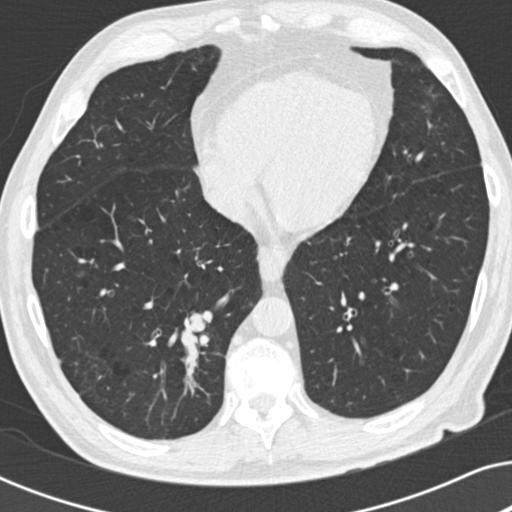
Low-dose screening chest CT, axial slice; baseline screening round; lung window (W 1500 / L -600 HU); 2 mm slice thickness; slice 112 of 191 in the series; 512 × 512 image matrix. Male participant, aged 73 years at enrolment.
Expert-annotated lung lesion, box from (x=156, y=293) to (x=226, y=369) px. The screening reader recorded 2 non-calcified nodules or masses ≥4 mm on this exam; which of them this box marks is not recorded. Official screen result: positive, change unspecified: nodule(s) >= 4 mm or enlarging nodule(s), mass(es), or other non-specific abnormalities suspicious for lung cancer. Participant outcome: lung cancer diagnosed 63 days after this screen — carcinoid tumor, NOS, right lower lobe, carcinoid, stage not assessed, 12 mm at pathology.